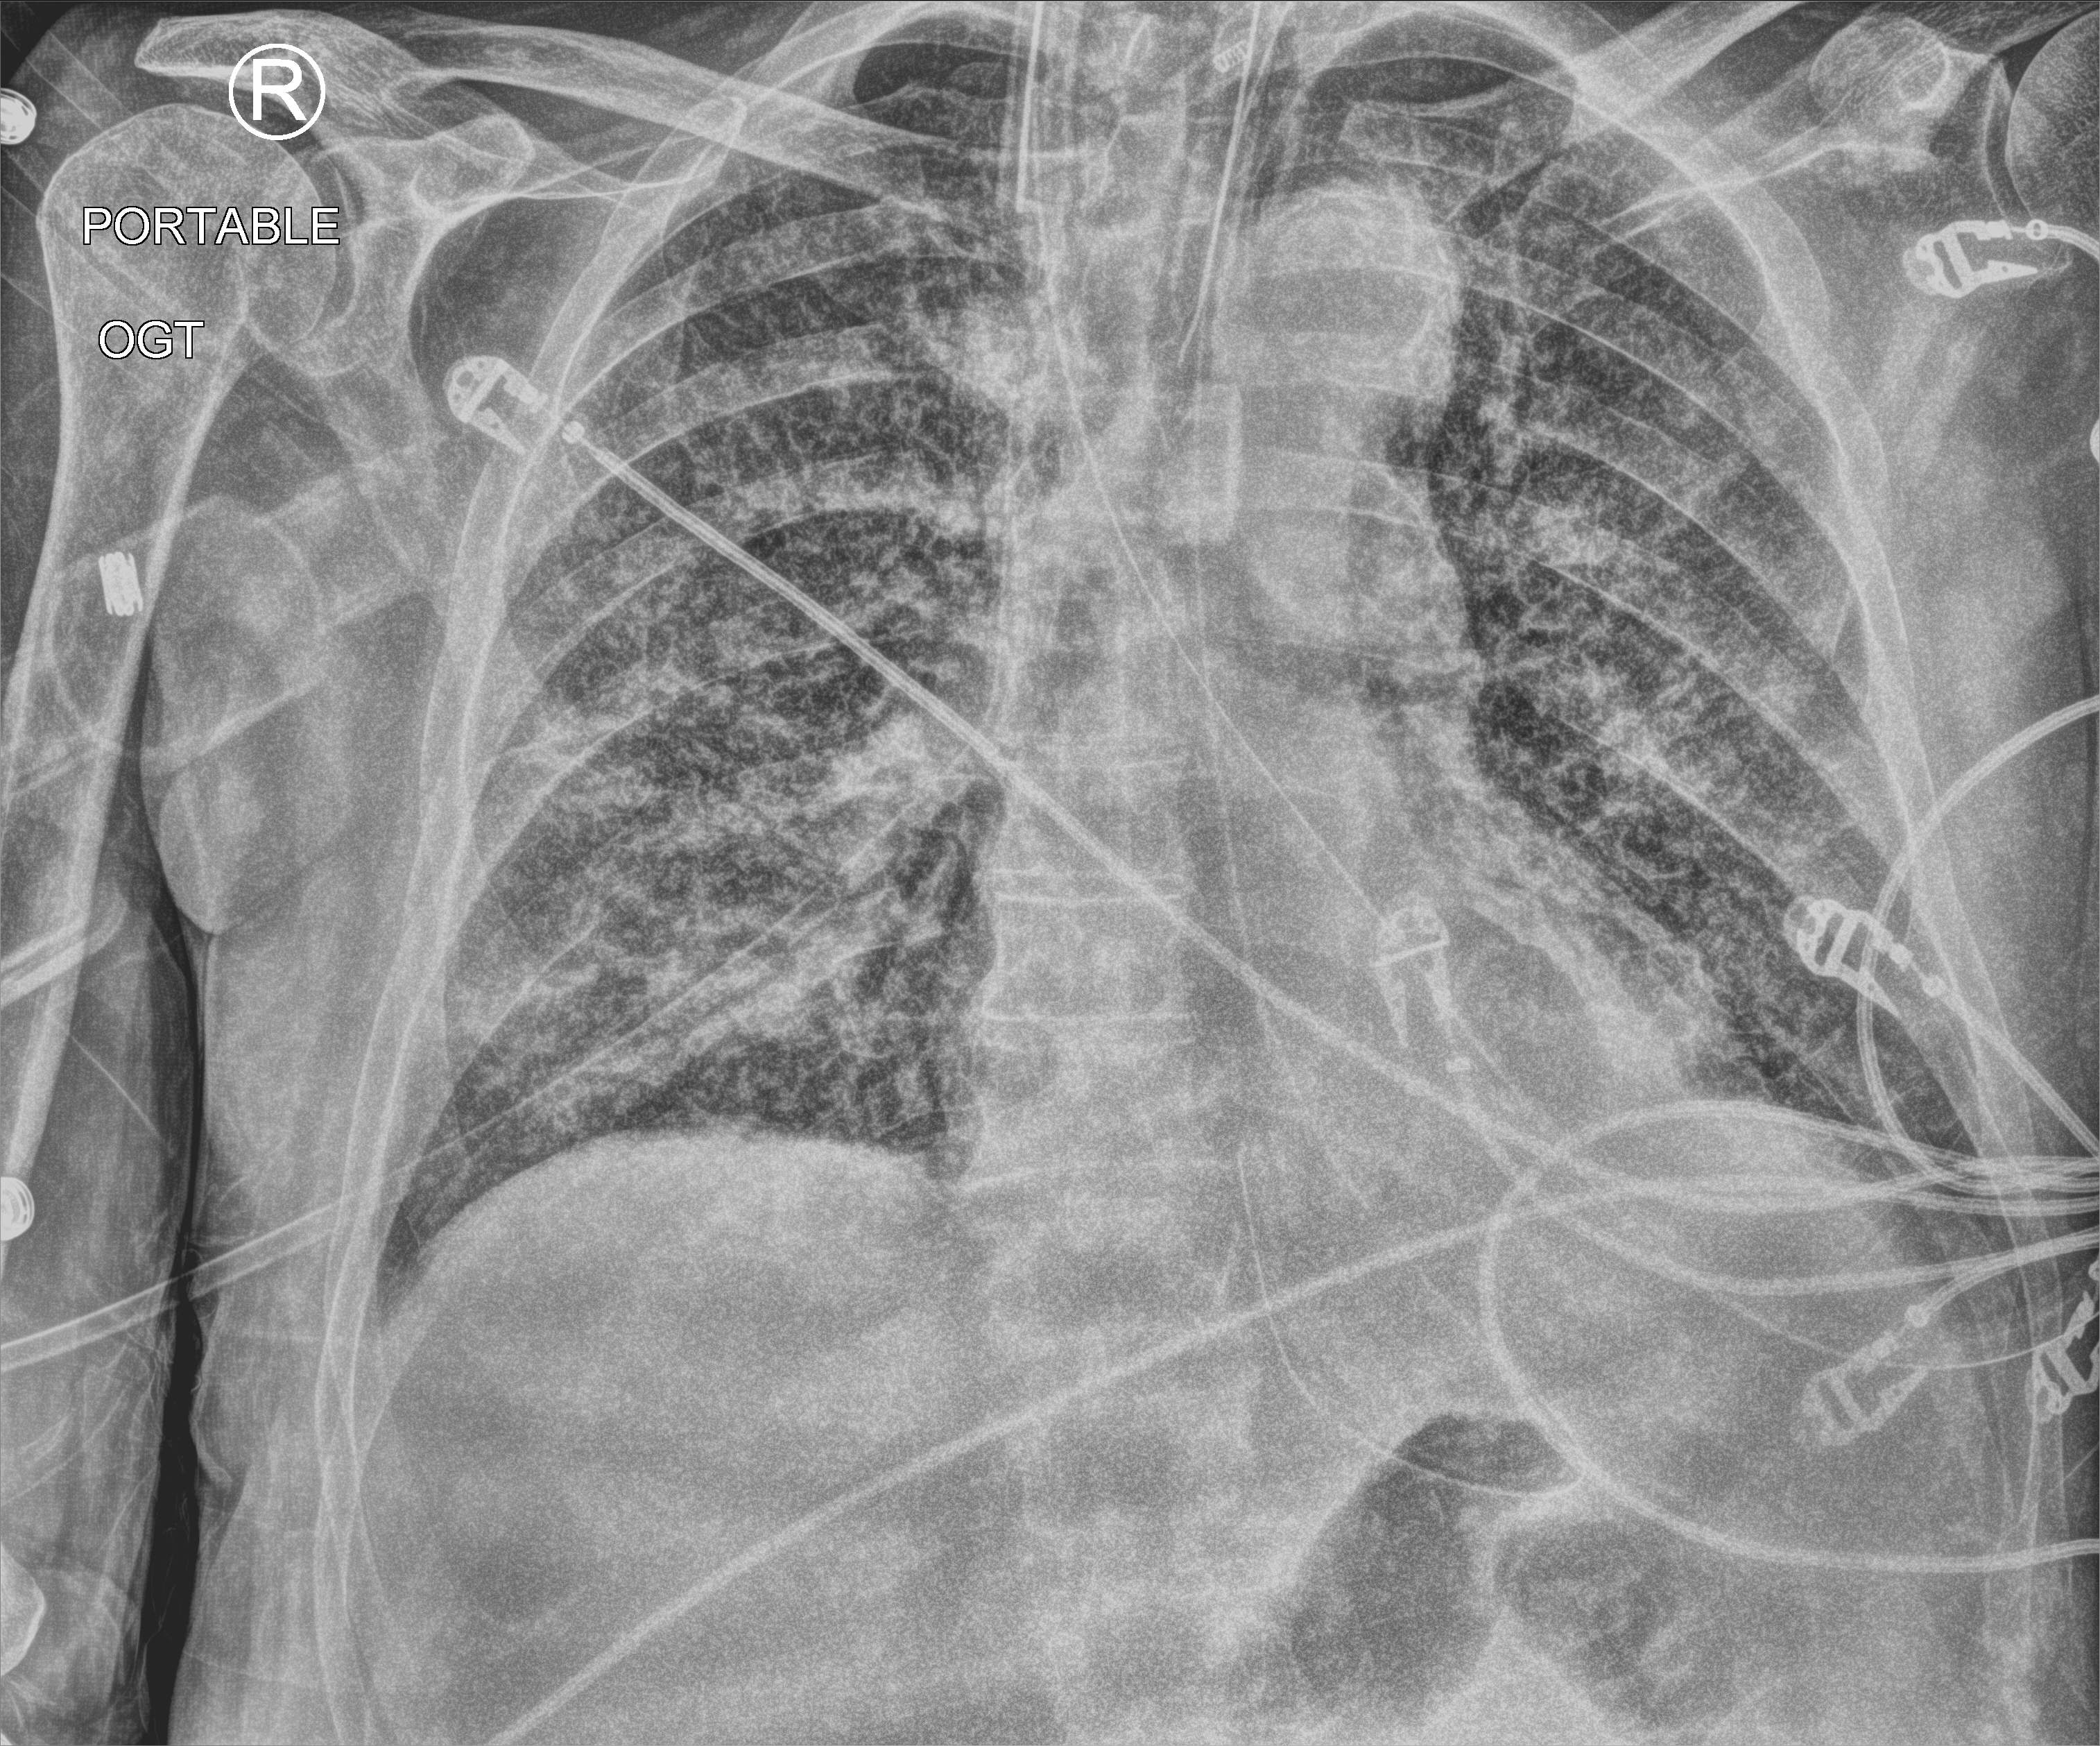
Portable chest radiograph, anteroposterior (AP) projection. Patient hospitalised with COVID-19; male, aged 75–90 years.
Admission-level facts for this patient (not findings on this image; timing relative to this image not recorded): mechanically ventilated during this hospital stay: yes; diabetes (admission record): no; other chronic lung disease (admission record): no.